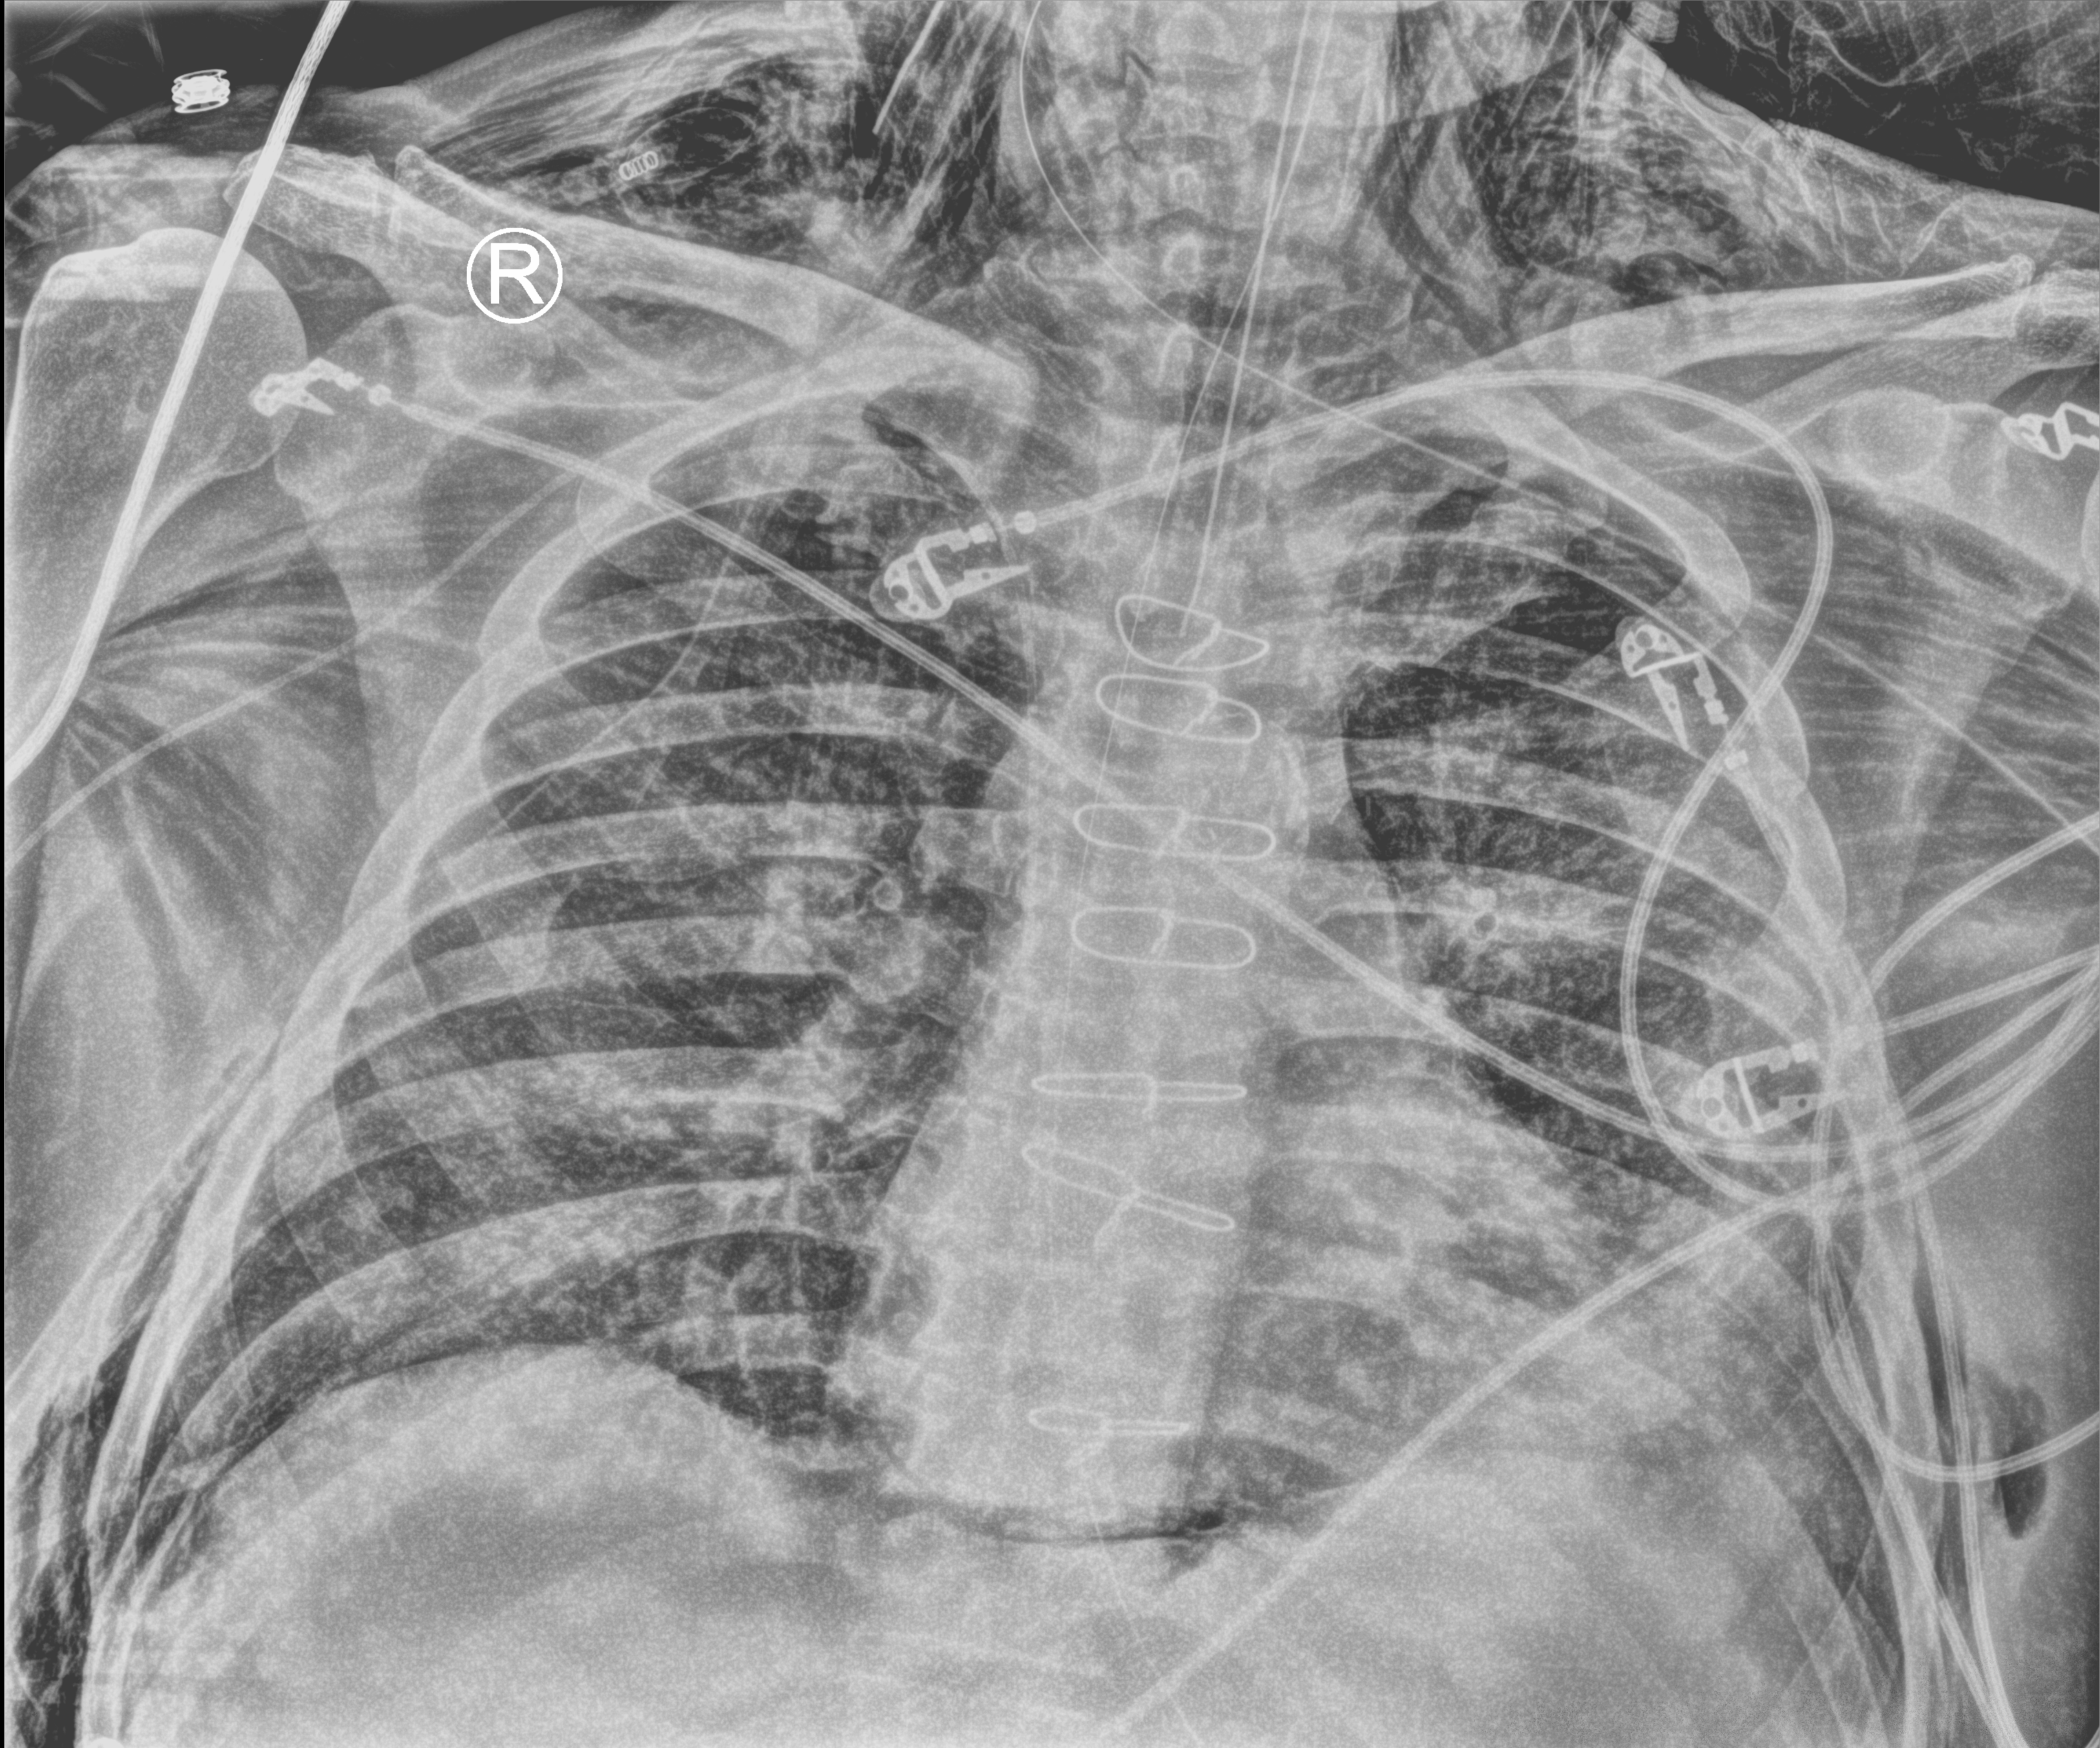
Bedside chest radiograph (computed radiography); anteroposterior (AP) projection. Male patient hospitalised with COVID-19, age 60–74 years.
From the hospital-stay record, not from the radiograph (when in the stay this image was taken is not recorded): smoking status (admission record): former.